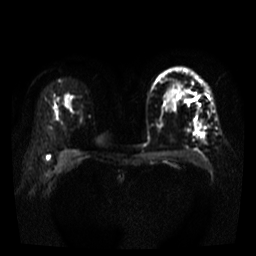
Breast MRI, one axial slice; position 26 of 35 along the scan axis; diffusion-weighted series; image 2 of 4 stored at this slice position (different b-values; order by instance number); 3 T; 256 × 256 image matrix, field of view 320 × 320 mm. Female patient.
Structures marked on this image (manually delineated by an expert):
- tumour on diffusion-weighted imaging: box from (x=197, y=122) to (x=200, y=129) px